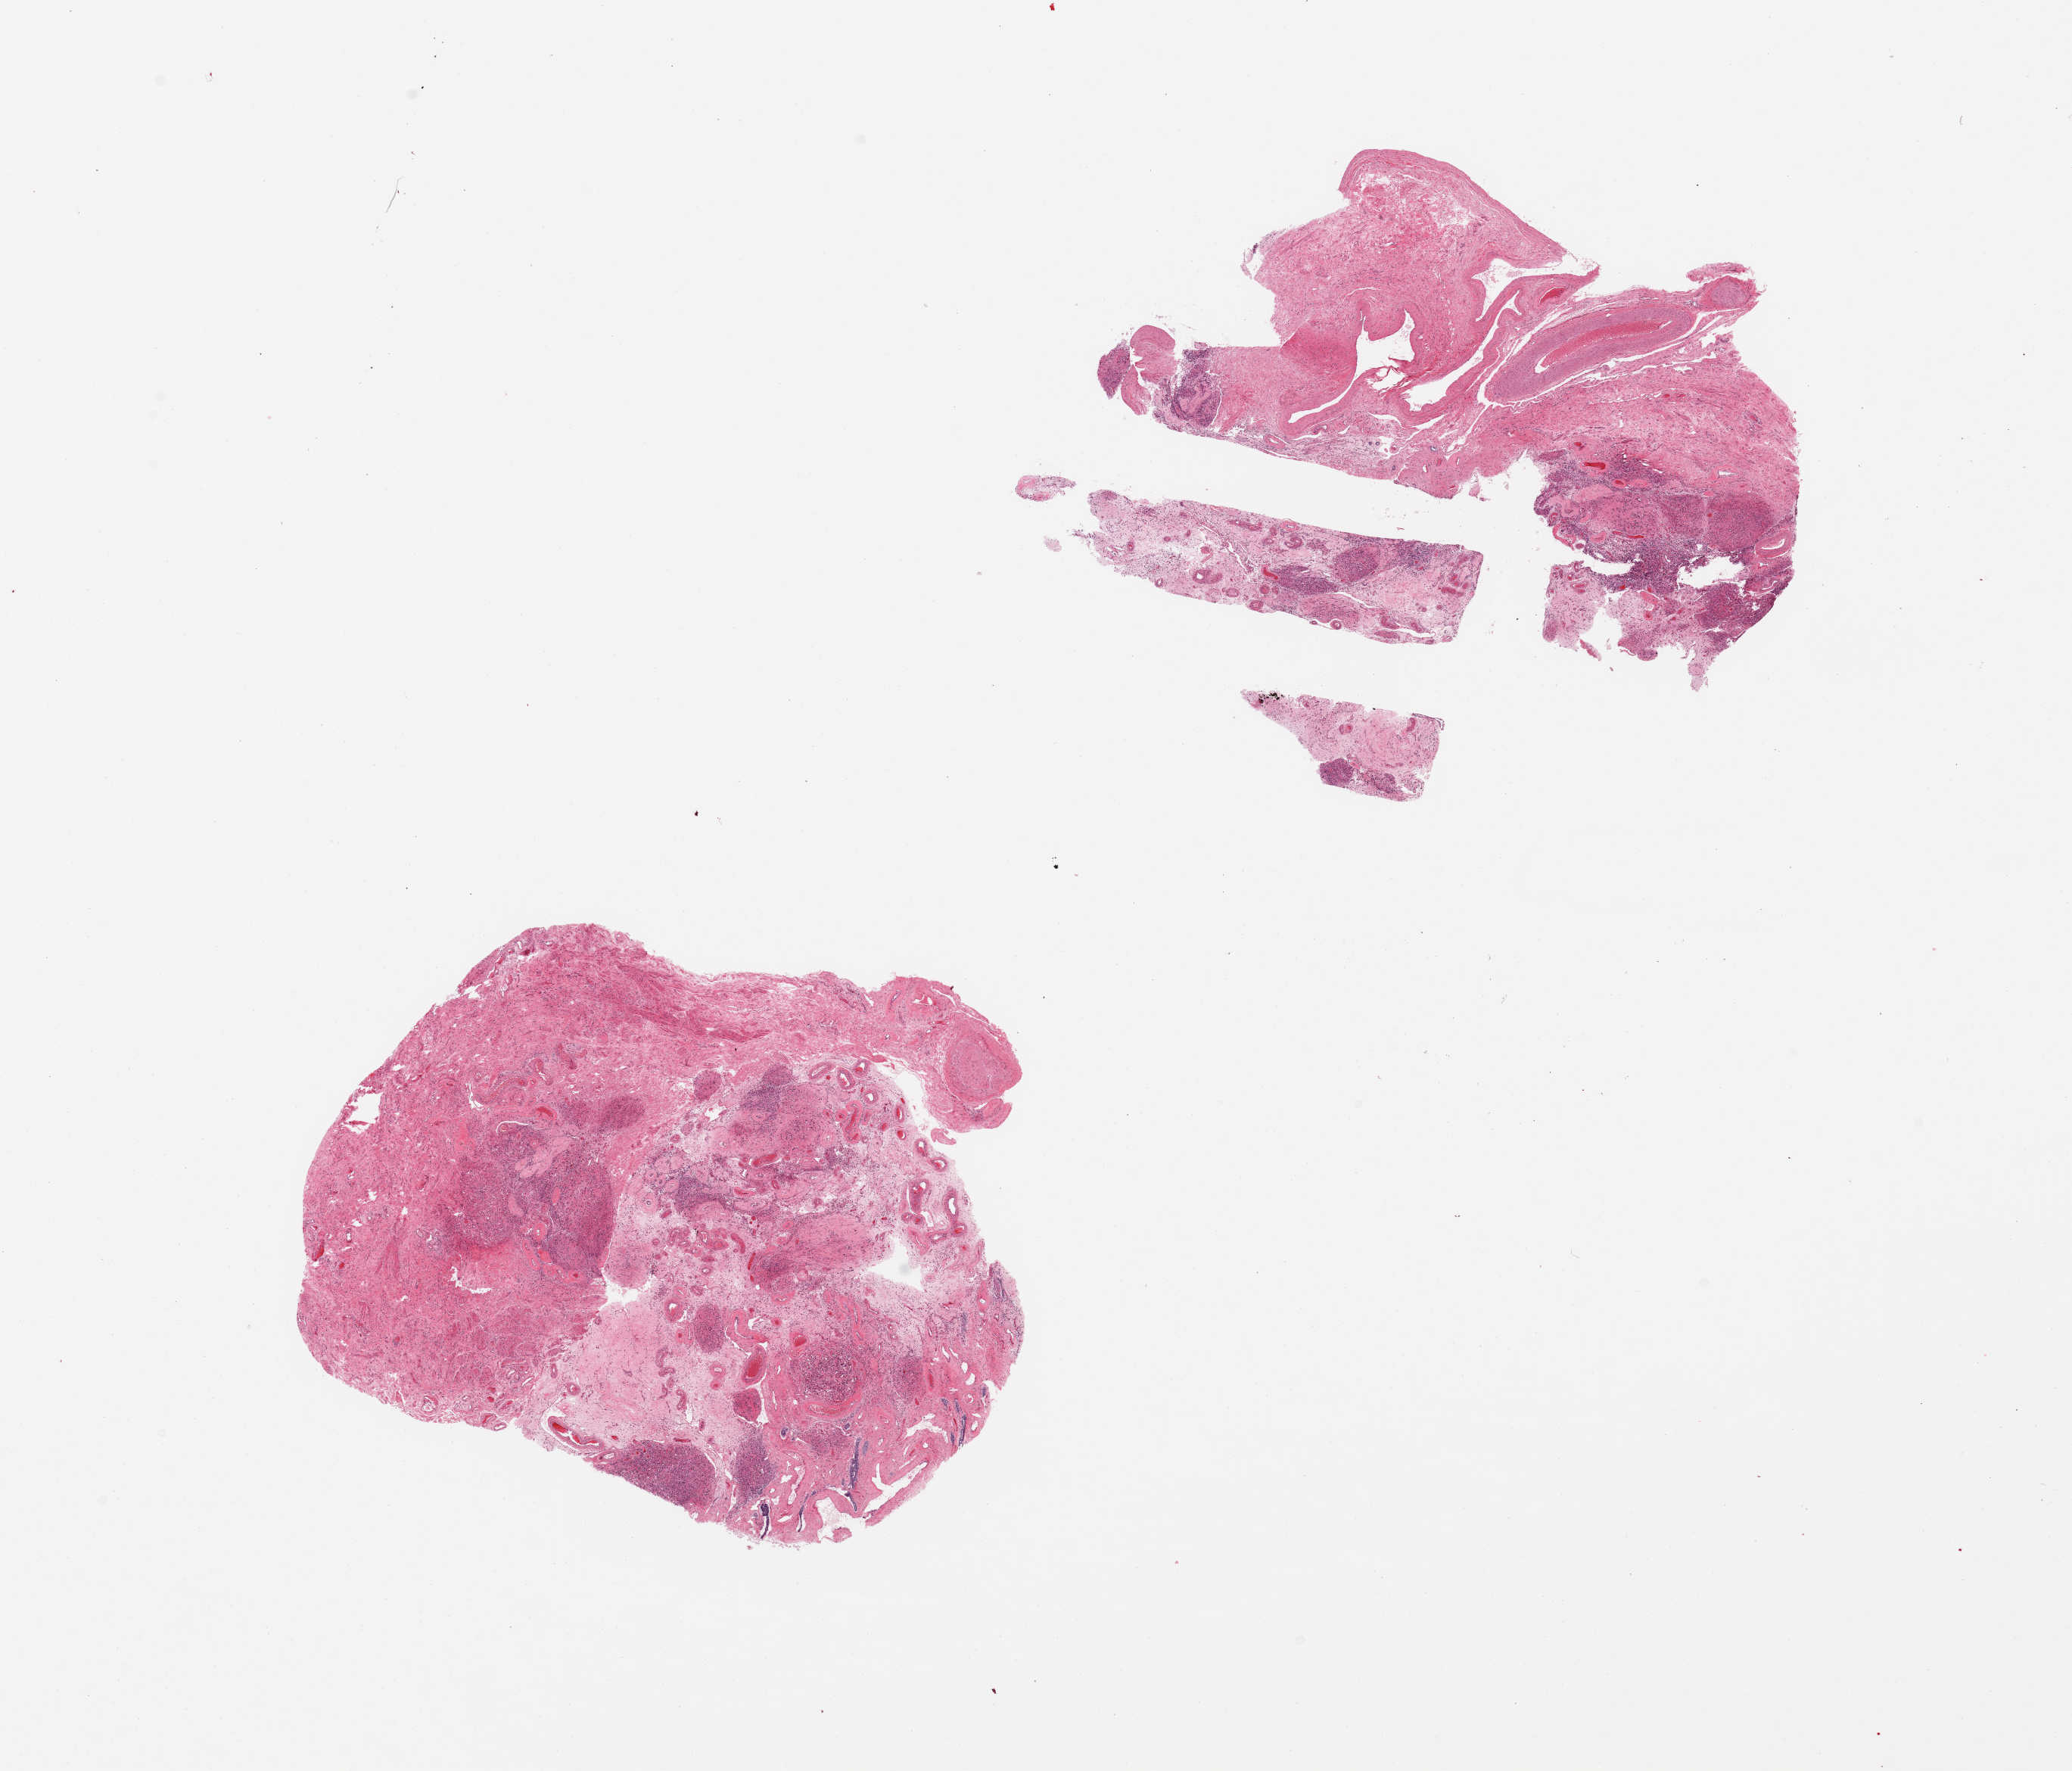
Digitized H&E-stained section, low-resolution overview of the scanned area, about 21.7 x 18.5 mm (acquisition: 20x scan), PAXgene-fixed paraffin-embedded (PFPE) section, section of testis (target tissue), donor tissue sample. Male donor.
Reviewer comment on this tissue sample: 2 pieces, seminiferous tubules with diffuse sclerotic atrophy, Leydig cell hyperplasia, pattern suggests Kleinfelter syndrome.